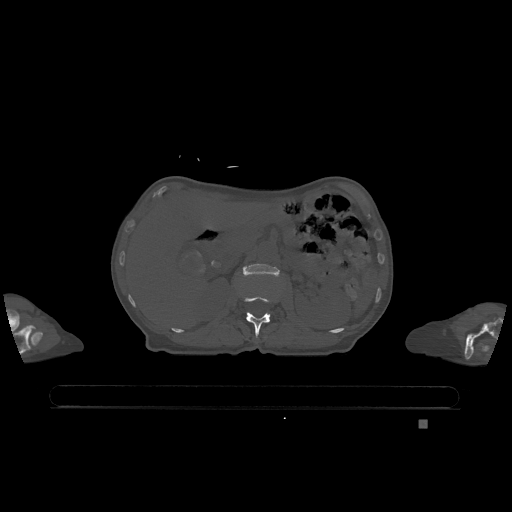
CT including the spine, one axial slice; position 460 of 1317 along the scan axis; bone window (W 1800 / L 400 HU); 512 × 512 image matrix, field of view 500 × 500 mm. Patient: female, 74 years. From the clinical record (not read from this slice): primary cancer: lung; vertebrae with lytic lesions (as recorded): T1, T4, T5, T6, L4, L5.
Outlined on this slice (semi-automatically segmented with operator editing):
- L1 vertebra: bounding box [x1, y1, x2, y2] px = [244, 296, 271, 337]
- L2 vertebra: [243, 264, 279, 276]